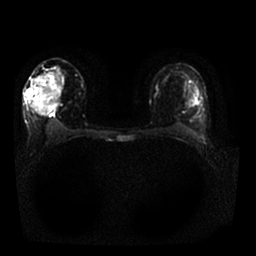
Breast MRI, one axial slice. Position 10 of 25 along the scan axis. Diffusion-weighted series; image 2 of 4 stored at this slice position (different b-values; order by instance number). 1.5 T. 256 × 256 image matrix. Female patient.
Structures marked on this image (expert manual segmentation):
- tumour on diffusion-weighted imaging: box from (x=25, y=88) to (x=34, y=97) px